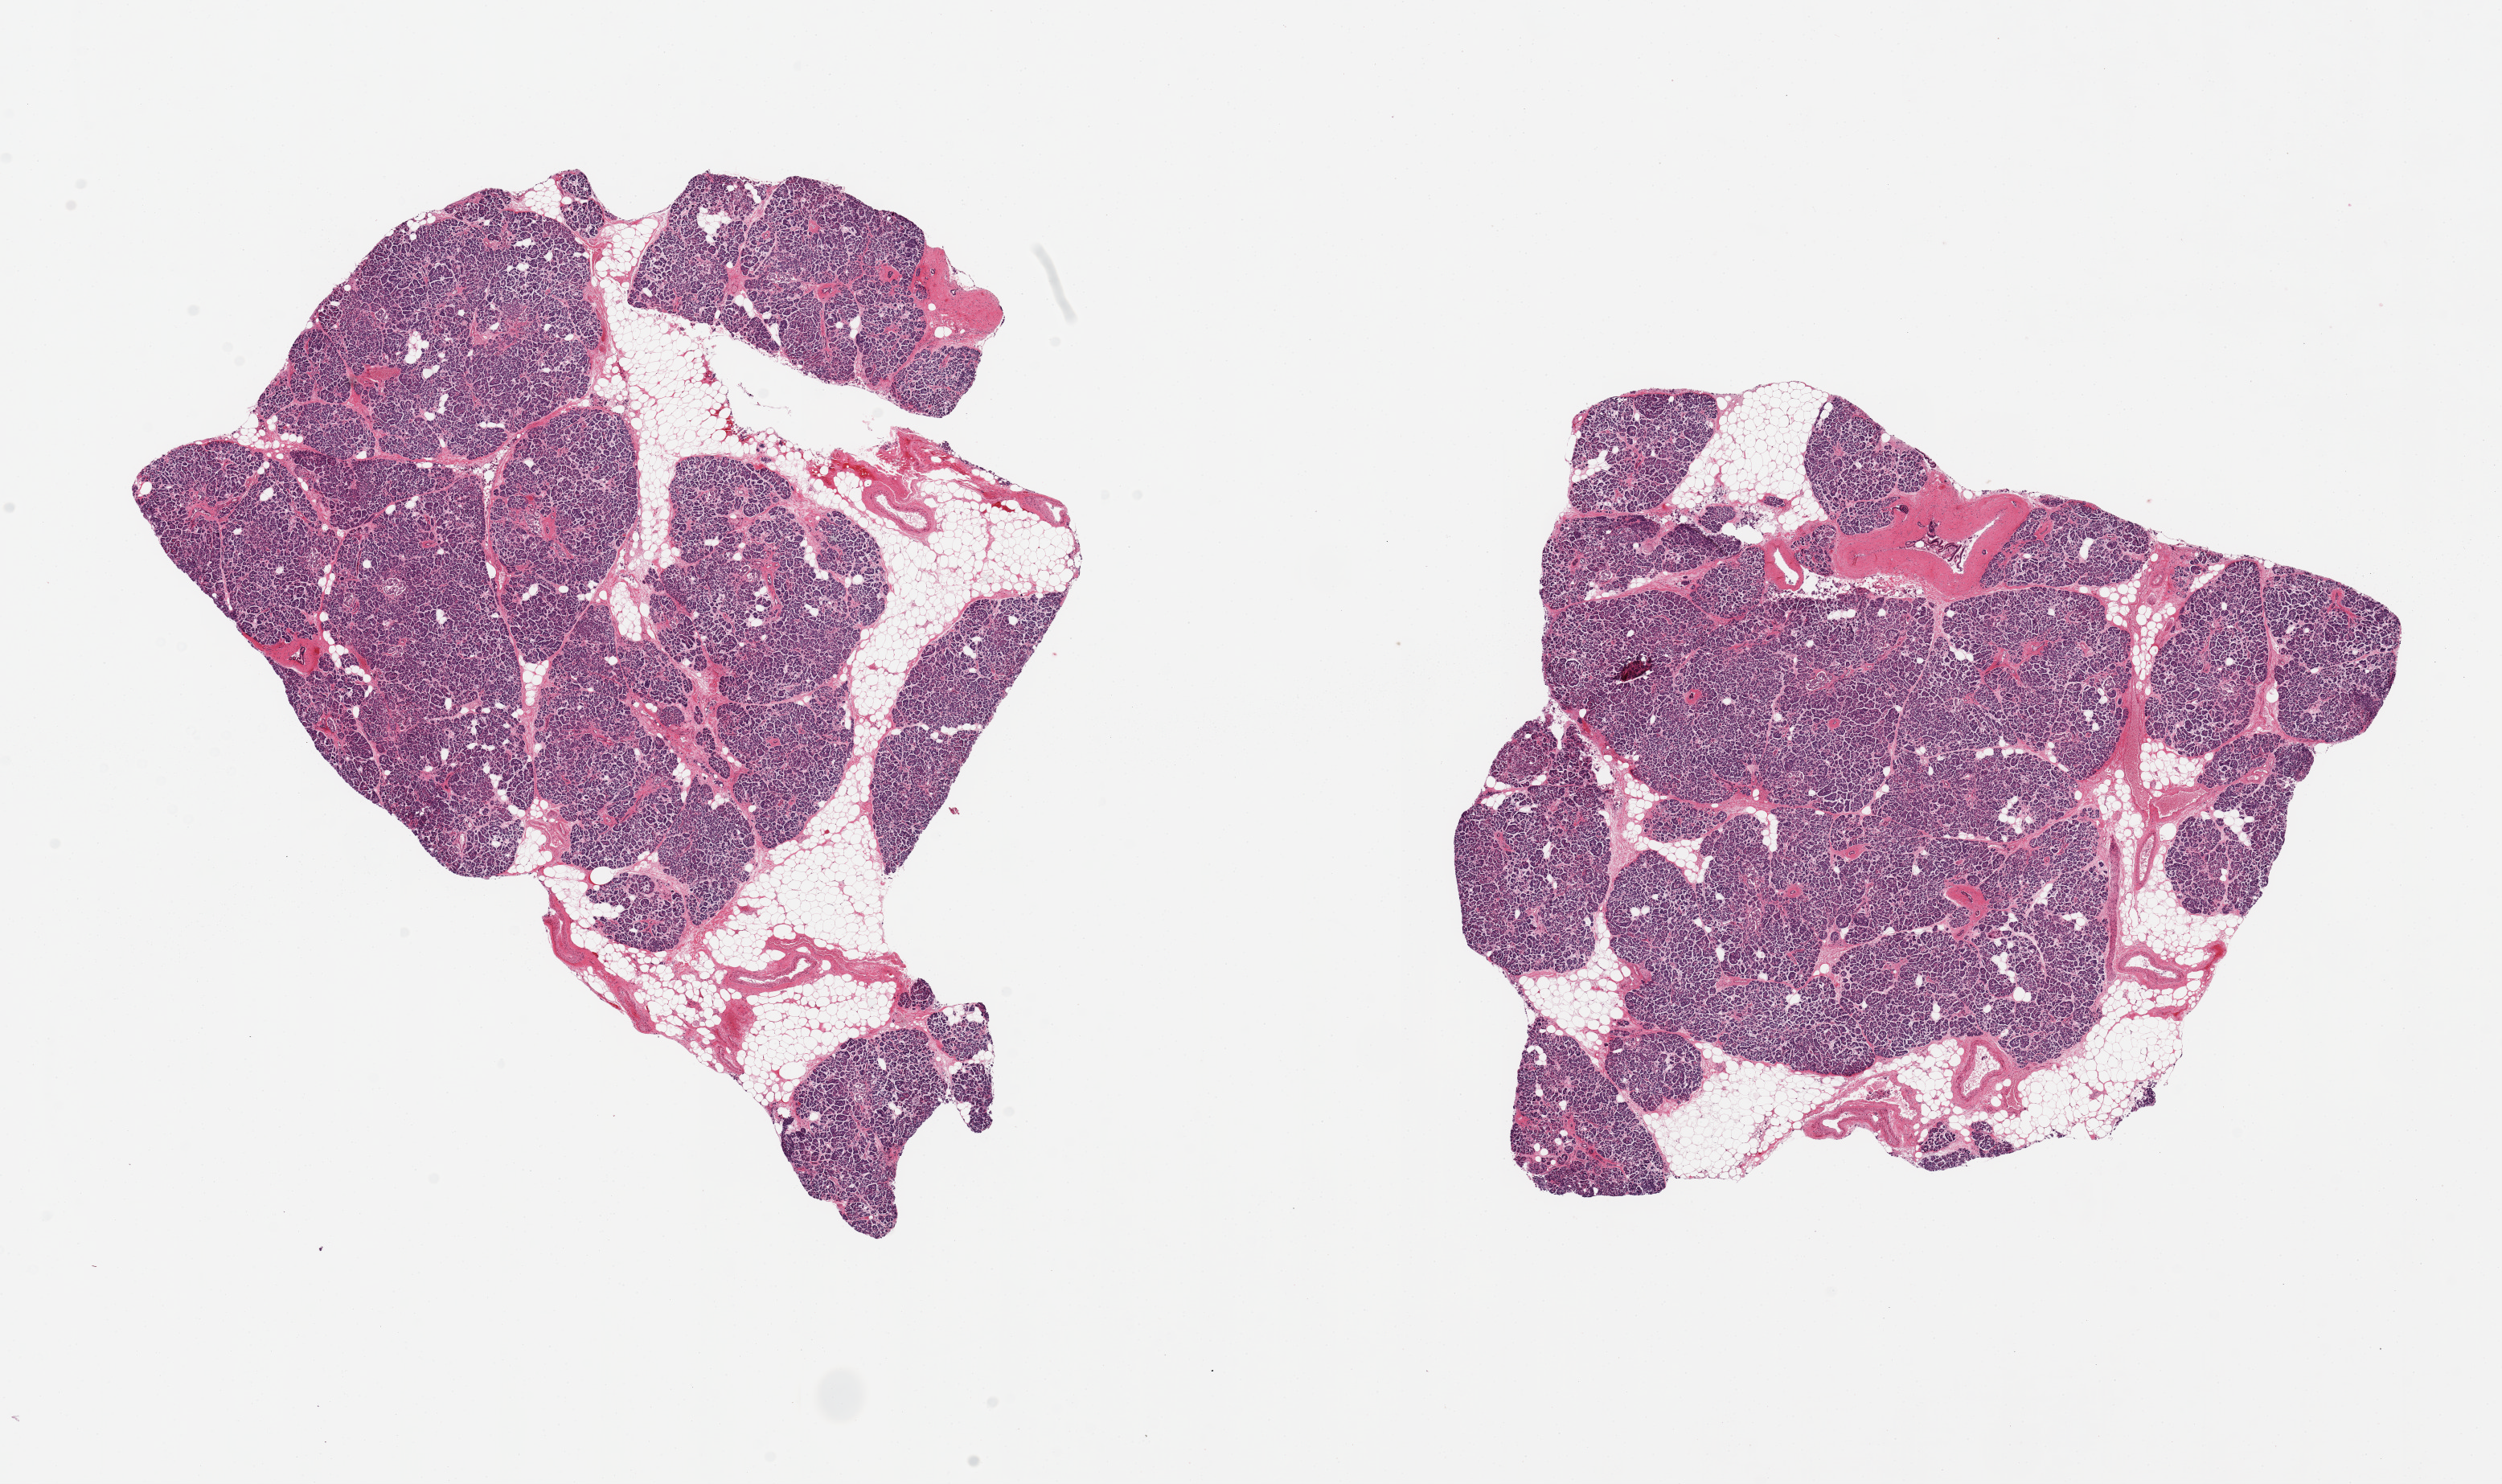
Digitized hematoxylin and eosin (H&E)-stained section, brightfield, low-resolution overview of the scanned area, about 24.6 x 14.6 mm; PAXgene-fixed paraffin-embedded (PFPE) section; target tissue: pancreas; tissue donor sample. Donor: female.
Pathologist's review note for this sample: 2 pieces. 10.5x8 & 9x8mm; 20% internal adipose.